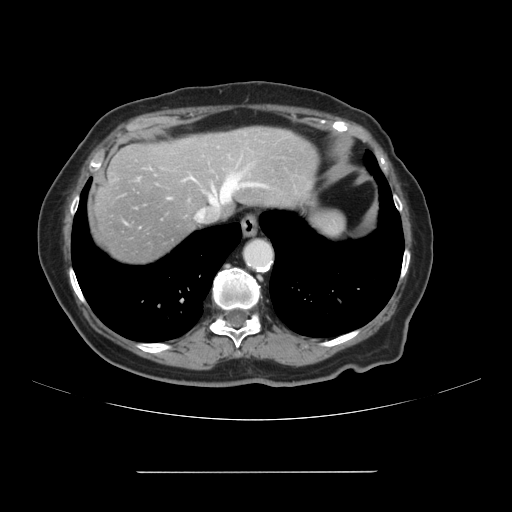
Contrast-enhanced abdominal CT, one axial slice. Position 94 of 111 along the scan axis. 120 kVp. Intravenous contrast given. Soft-tissue window (W 400 / L 40 HU). 2.5 mm slice thickness. 512 × 512 image matrix, field of view 400 × 400 mm. Female patient, age 74 years. From the clinical record (not read from this slice): diagnosis: colorectal cancer liver metastases, imaged before liver resection; multiple liver metastases: yes; largest metastasis: 1.1 cm; disease in both lobes: yes.
Outlined on this slice (outlined manually by an expert reader):
- hepatic veins: box from (x=210, y=176) to (x=256, y=206) px
- liver: (x=92, y=127)–(x=317, y=266)
- planned liver remnant (the part of the liver to remain after resection): (x=179, y=127)–(x=318, y=213)
- portal vein (with intrahepatic branches): (x=212, y=194)–(x=220, y=199)
- liver metastasis: (x=109, y=174)–(x=116, y=181)